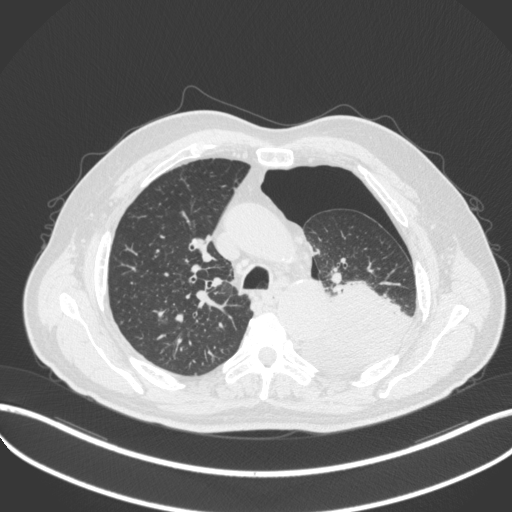
Chest CT, one axial slice; slice 360 of 466 in the series (ordered by position); reconstruction kernel B31f; 120 kVp; lung window (W 1500 / L -600 HU); 512 × 512 image matrix, field of view 400 × 400 mm. Patient: male, 76 years. From the clinical record (not read from this slice): clinical TNM (as recorded): T3 N0 M1b.
Outlined on this slice (rectangle marked by the reading radiologist):
- lung tumour (recorded histology: adenocarcinoma): bounding box [x1, y1, x2, y2] px = [294, 278, 417, 365]